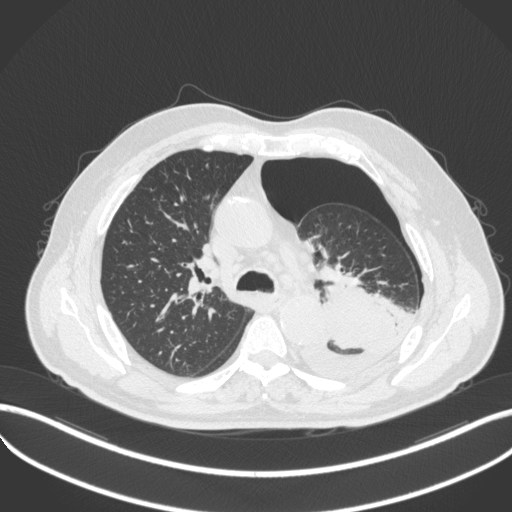
Chest CT, one axial slice. Position 341 of 466 along the scan axis. Reconstruction kernel B31f. Lung window (W 1500 / L -600 HU). 1 mm slice thickness. 512 × 512 image matrix. Patient: male, 76 years. From the clinical record (not read from this slice): clinical TNM (as recorded): T3 N0 M1b.
Annotated regions visible in this slice (rectangle marked by the reading radiologist):
- lung tumour (recorded histology: adenocarcinoma): bounding box <290,281,401,386> (left, top, right, bottom; pixels)